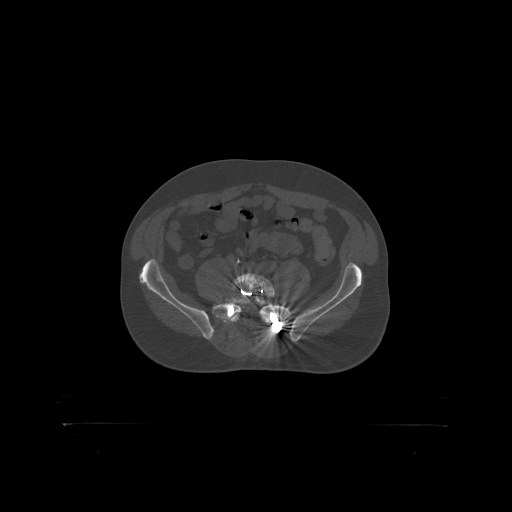
CT including the spine, one axial slice. Position 193 of 399 along the scan axis. 120 kVp. Bone window (W 1800 / L 400 HU). 1.25 mm slice thickness. 512 × 512 image matrix, field of view 650 × 650 mm. Male patient, age 46 years. From the clinical record (not read from this slice): primary cancer: skin.
Structures marked on this image (semi-automatic segmentation, software-assisted and operator-edited):
- L5 vertebra: box from (x=232, y=274) to (x=275, y=298) px